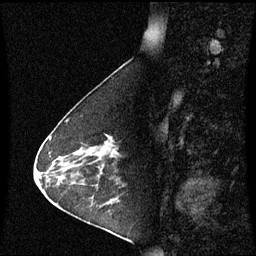
Breast MRI (dynamic contrast-enhanced), one sagittal slice; position 23 of 60 along the scan axis; dynamic contrast-enhanced series, image 2 of 3 at this slice position (ordered by acquisition); 1.5 T; TE 4.2 ms, TR 8.9 ms; 2 mm slice thickness; 256 × 256 image matrix. Patient: female, 63 years. Case-level facts recorded for this patient, not image findings: setting: breast cancer imaged before/during neoadjuvant chemotherapy; receptor status: HR-positive, HER2-negative.
Annotated regions visible in this slice (semi-automatically segmented with operator editing):
- analysis volume of interest (the breast-tissue region the enhancement analysis was run in; not a lesion): bounding box (x1, y1, x2, y2) in pixels: (76, 136, 120, 178)
- tumour enhancement mask (voxels above the 70 % enhancement threshold inside the analysis volume of interest): (109, 137, 117, 158)